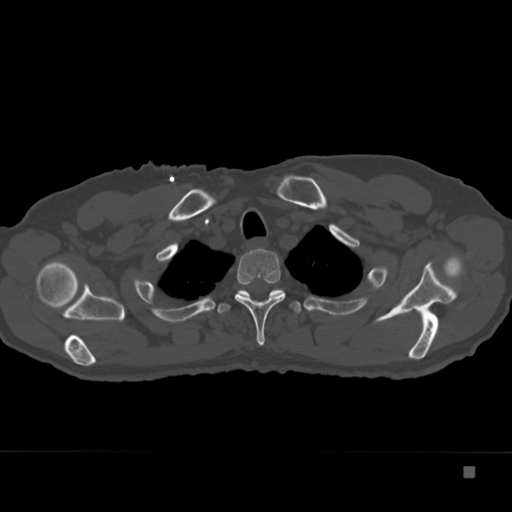
CT including the spine, one axial slice. 120 kVp. Bone window (W 1800 / L 400 HU). 512 × 512 image matrix. Patient: male, 72 years. From the clinical record (not read from this slice): primary cancer: skeletal.
Structures marked on this image (semi-automatically segmented with operator editing):
- T2 vertebra: box from (x=235, y=248) to (x=285, y=346) px
- T3 vertebra: (x=217, y=289)–(x=302, y=314)